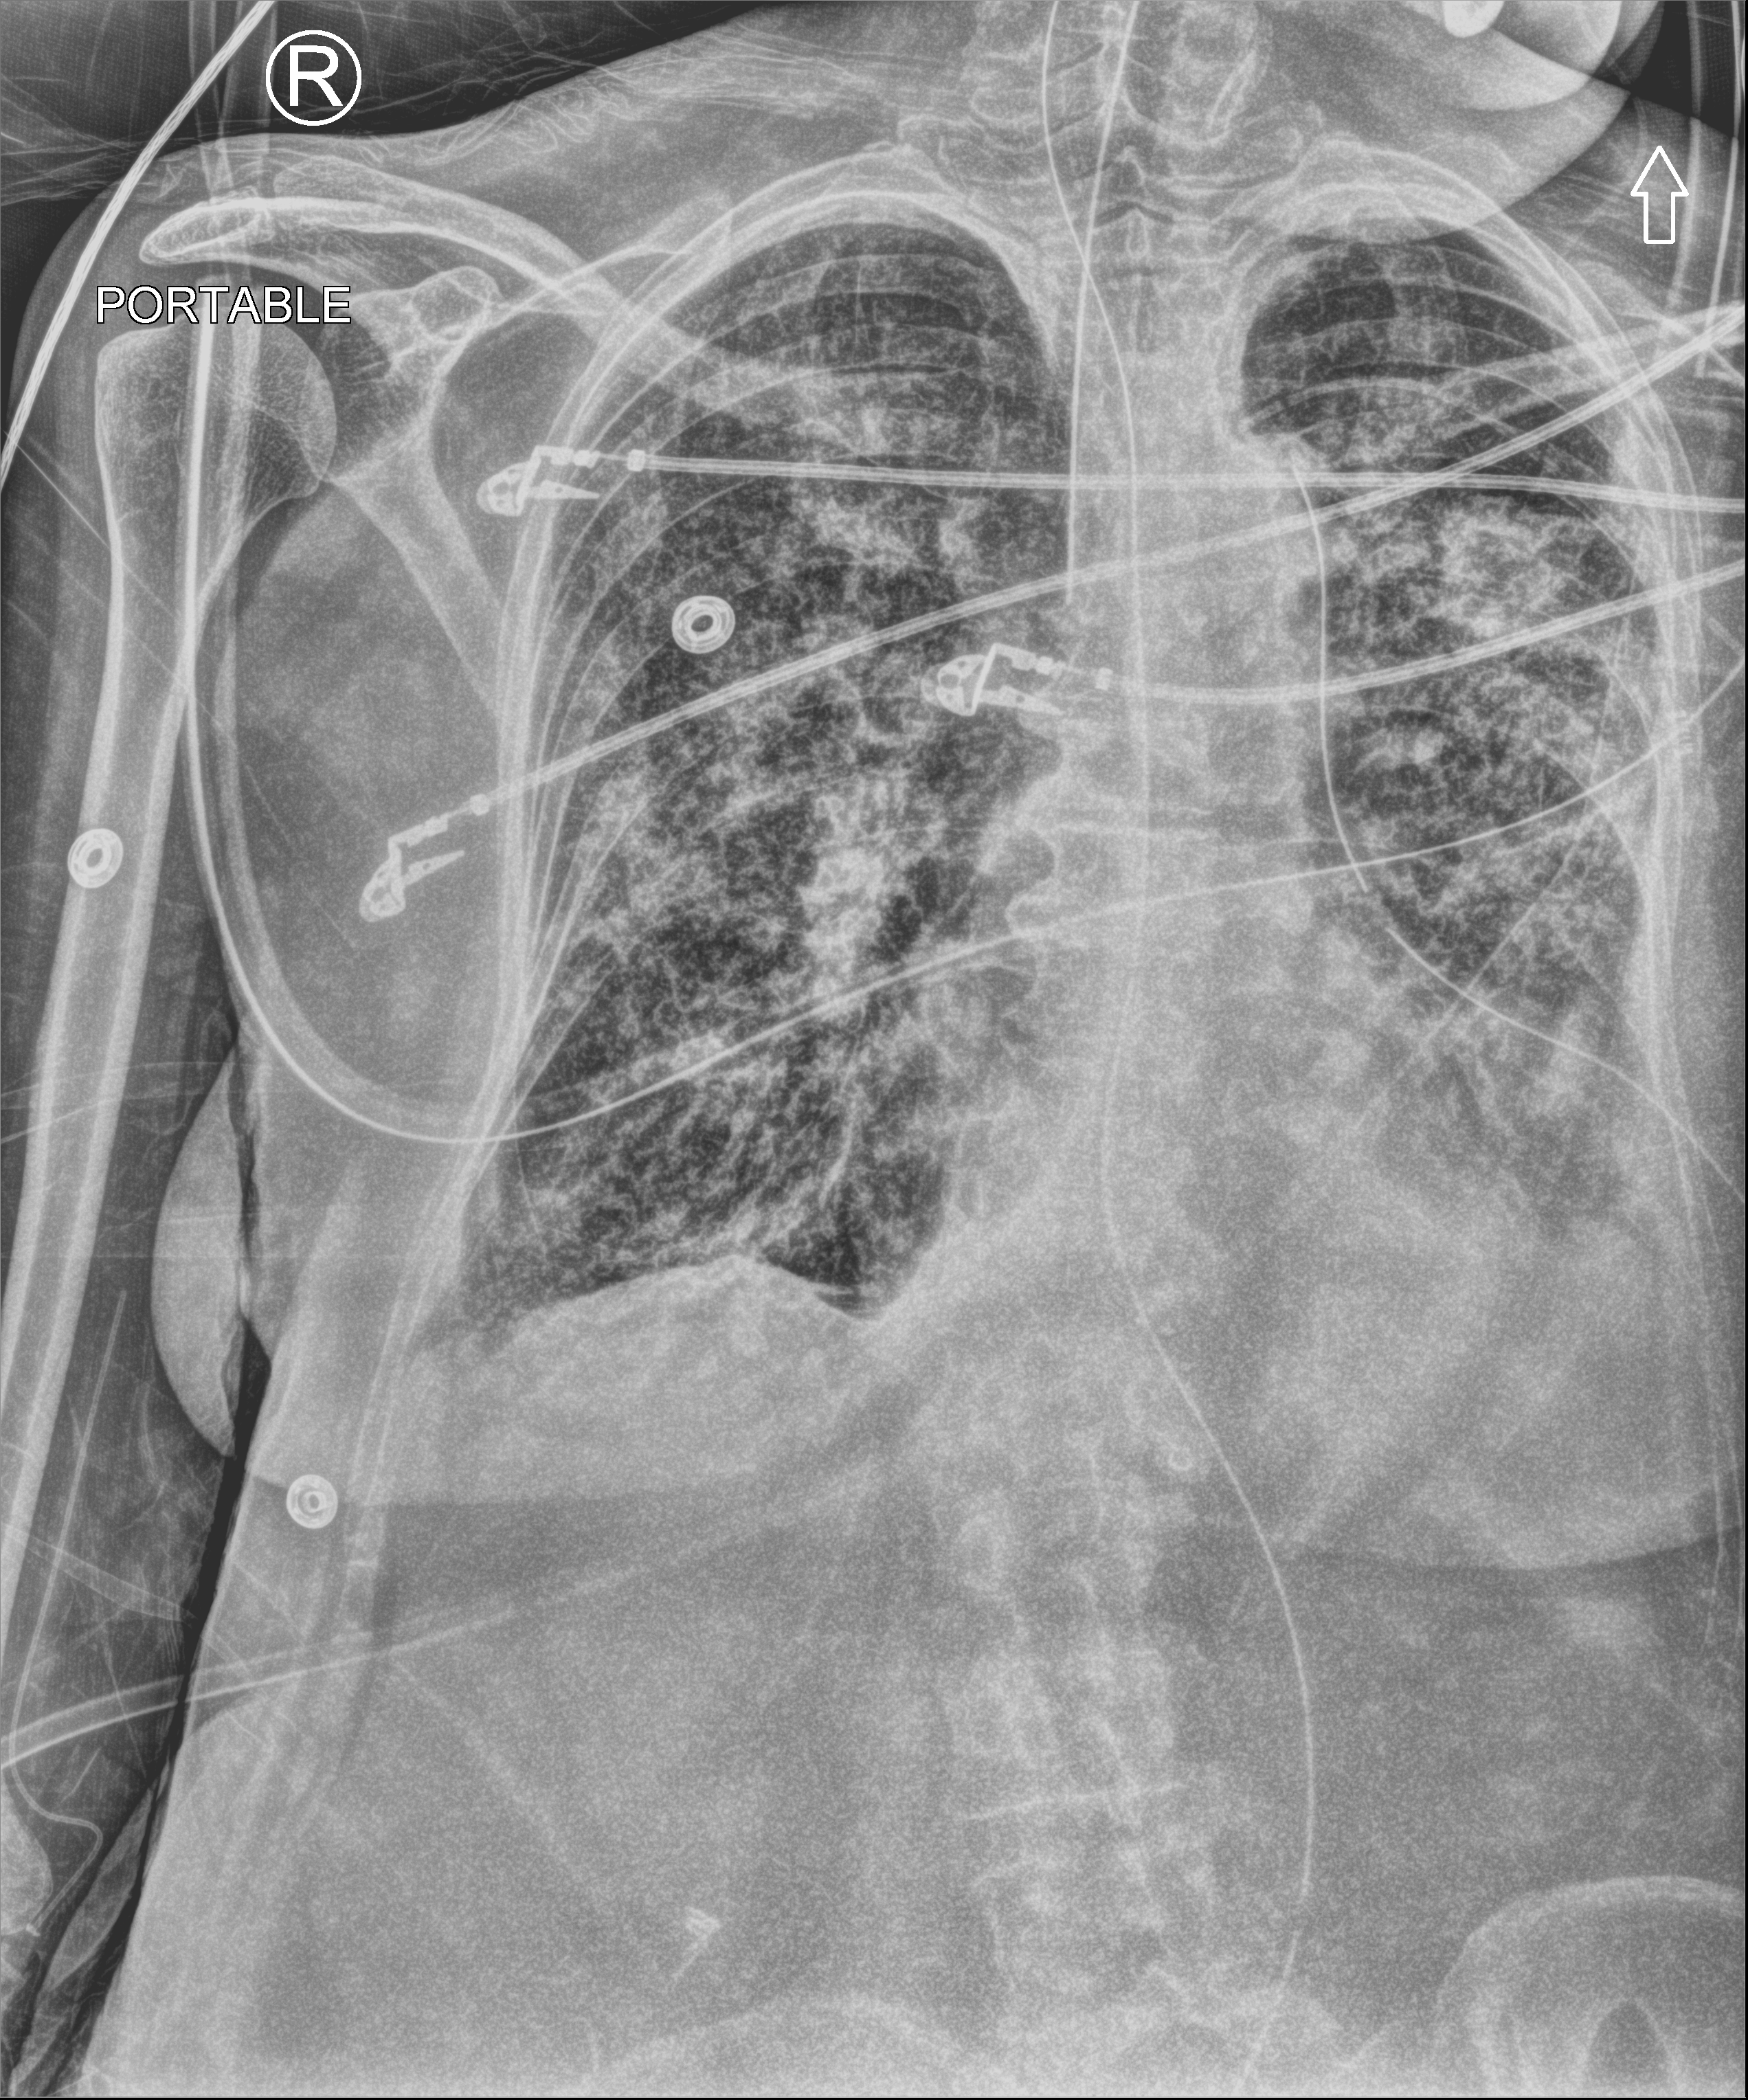
Bedside chest radiograph (computed radiography), anteroposterior (AP) projection. Female patient hospitalised with COVID-19, age 75–90 years.
Admission-level facts for this patient (not findings on this image; timing relative to this image not recorded): other chronic lung disease (admission record): yes; admitted to intensive care during this hospital stay: yes; mechanically ventilated during this hospital stay: yes.